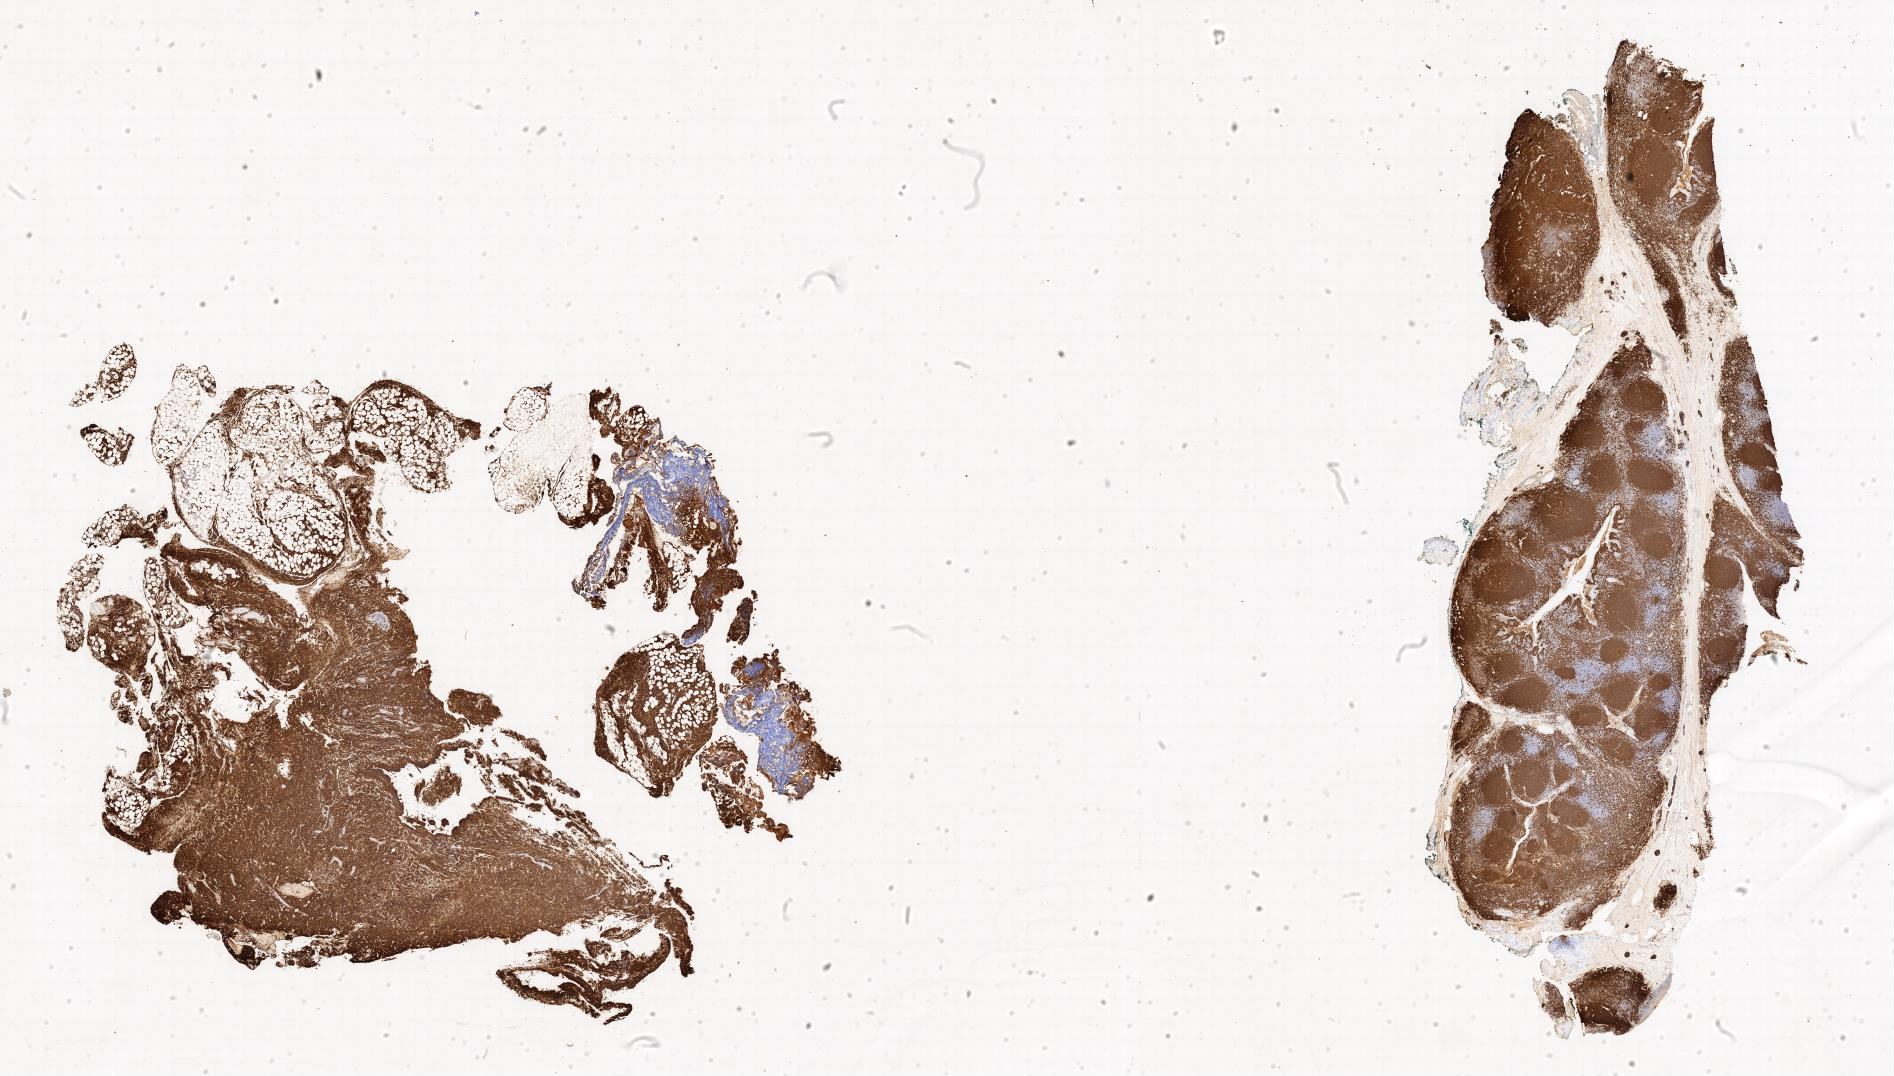
IHC for CD20, whole-slide image, shown as a low-resolution overview of the whole scanned area; specimen: tumor tissue; site: abdominal lymph node. Patient: male, age at initial diagnosis 9 years.
* histologic diagnosis: Burkitt lymphoma, NOS